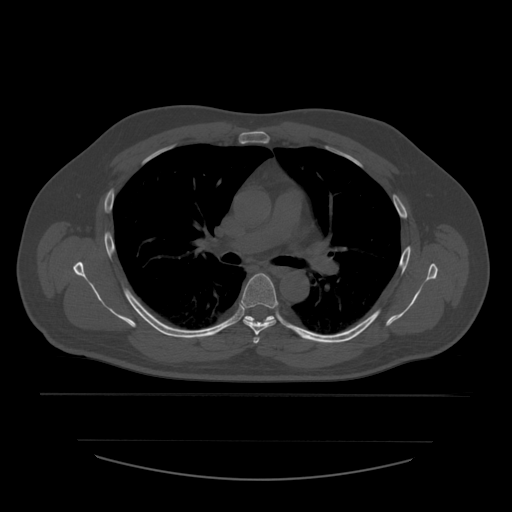
CT including the spine, one axial slice. Position 394 of 532 along the scan axis. Reconstruction kernel STANDARD. 120 kVp. Bone window (W 1800 / L 400 HU). 1.25 mm slice thickness. 512 × 512 image matrix, field of view 441 × 441 mm. Patient age 44 years. From the clinical record (not read from this slice): primary cancer: soft tissue sarcoma.
Structures marked on this image (semi-automatically segmented with operator editing):
- T4 vertebra: bounding box <253,337,260,344> (left, top, right, bottom; pixels)
- T5 vertebra: <241,273,279,336>
- T6 vertebra: <245,316,274,321>